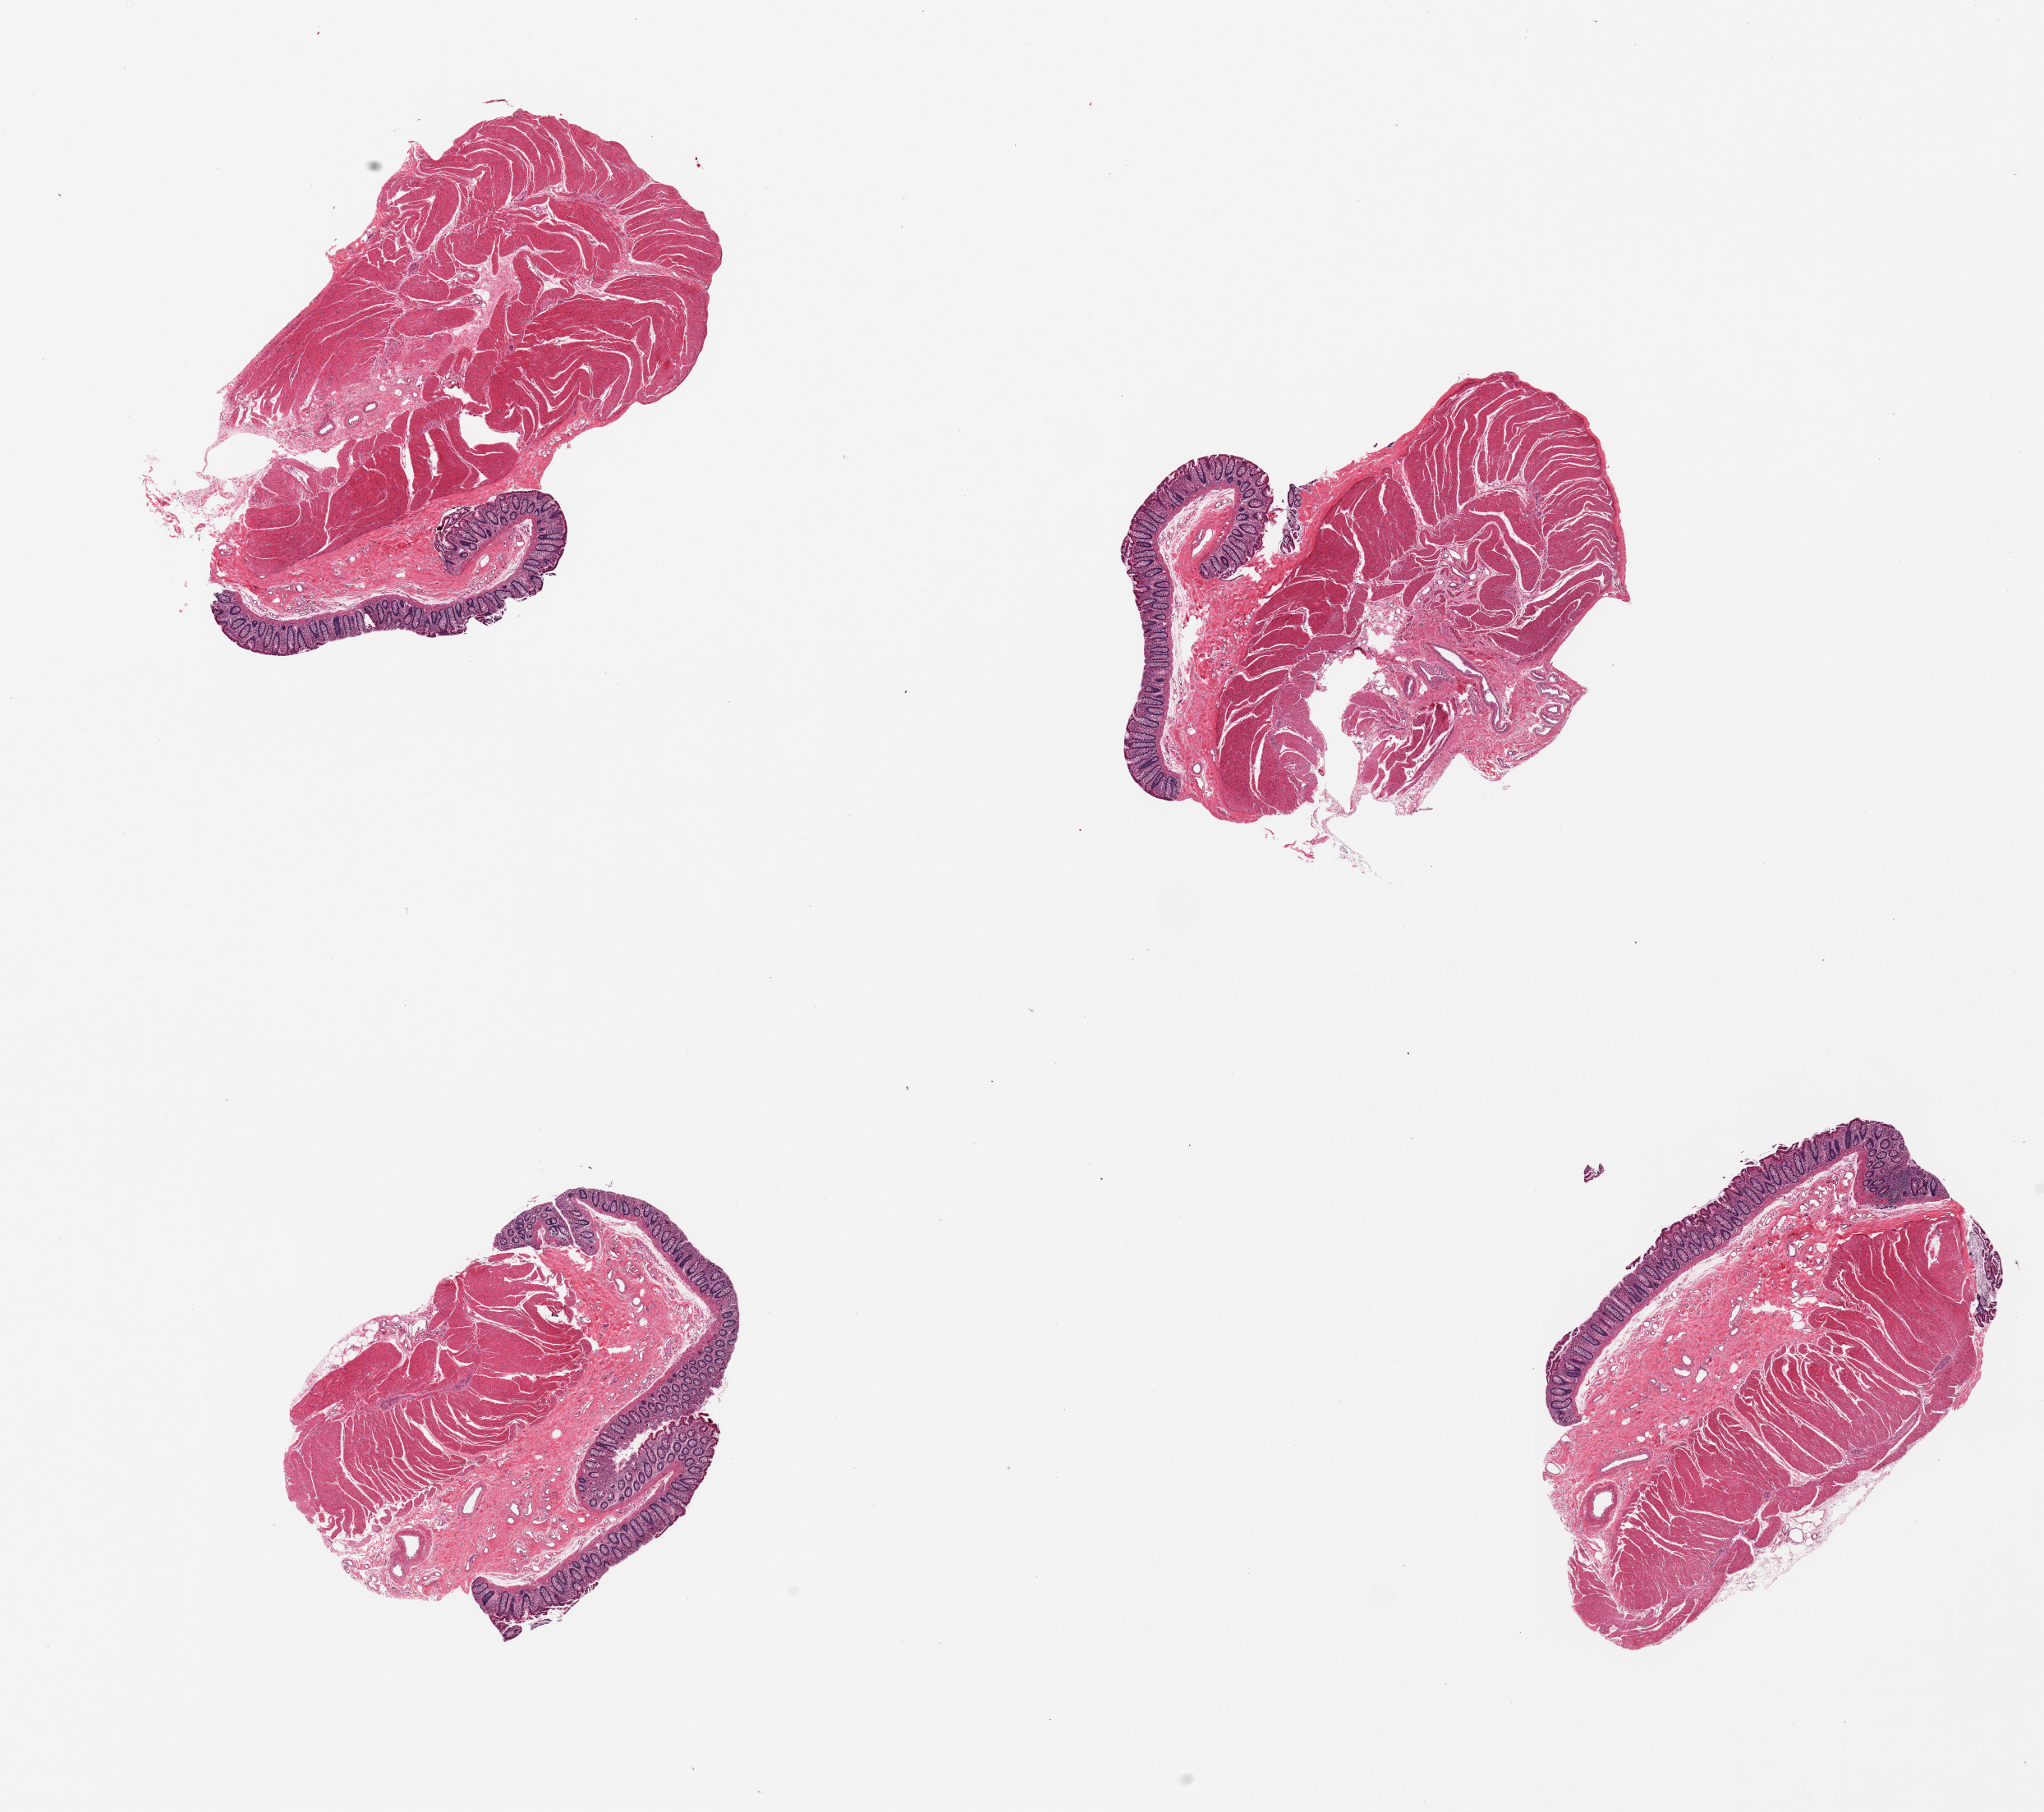
Haematoxylin and eosin whole-slide image, brightfield, shown as a low-resolution overview of the whole scanned area (about 19.7 x 17.5 mm). PAXgene-fixed, paraffin-embedded tissue. Section of transverse colon (target tissue). Donor tissue sample. Donor: female.
* reviewer comment on this tissue sample: 4 pieces, well preserved, mucosa is ~0.3mm thick, ~10% thickness